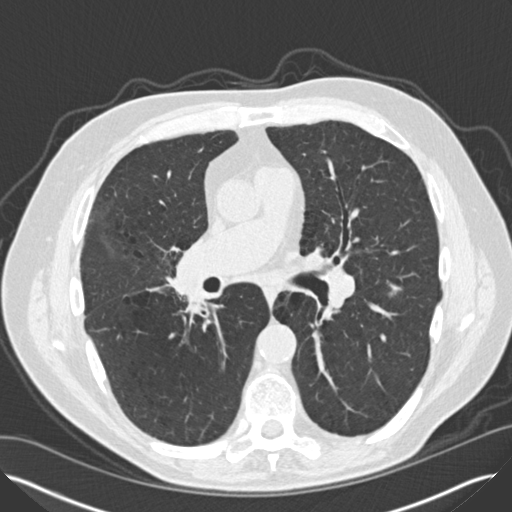
Low-dose screening chest CT, one axial slice. Position 77 of 149 along the scan axis. Lung window (W 1500 / L -600 HU). 2 mm slice thickness. 512 × 512 image matrix, field of view 370 × 370 mm.
Structures marked on this image (expert manual segmentation):
- lesion 1 (tumor, lower lobe of left lung): bounding box (x1, y1, x2, y2) in pixels: (390, 288, 402, 296)
- lesion 2 (tumor, hilum of right lung): (188, 279, 206, 302)